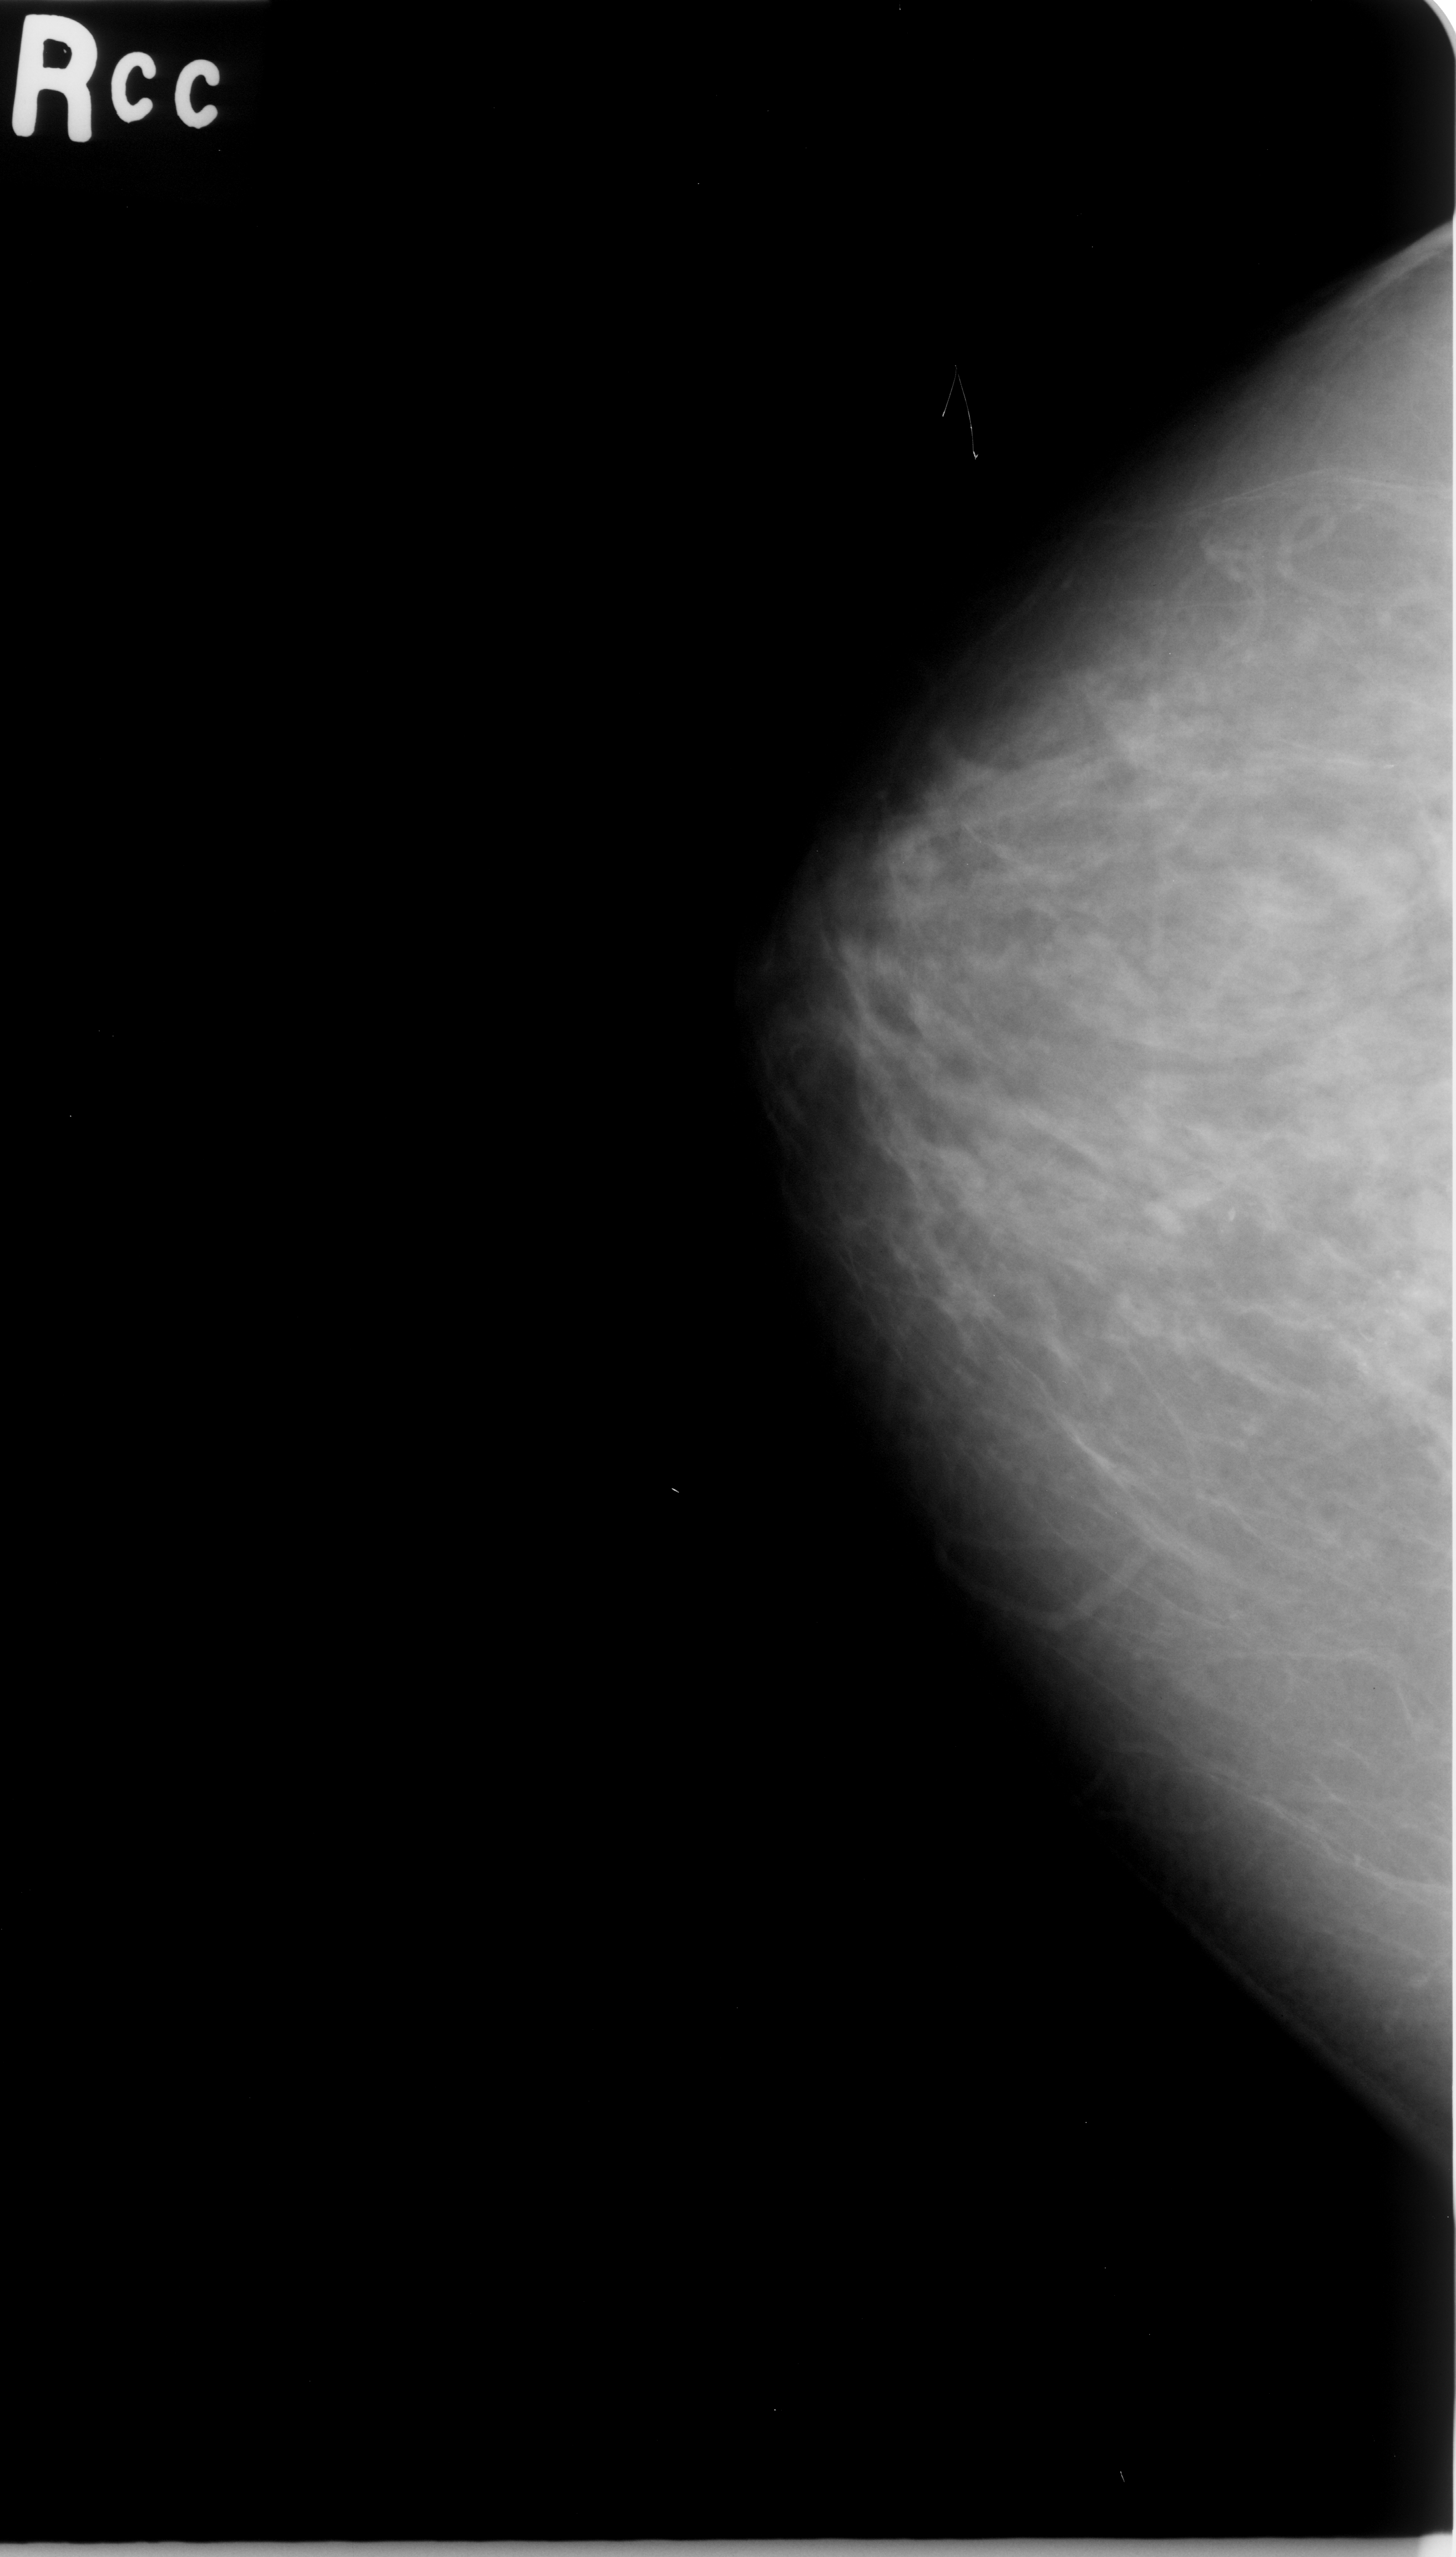
Mammogram (digitized film), right breast, craniocaudal (CC) view, BI-RADS breast density category 2 (scale 1–4).
Calcifications, morphology pleomorphic, distribution clustered; BI-RADS assessment category 5; pathology (as recorded): malignant.